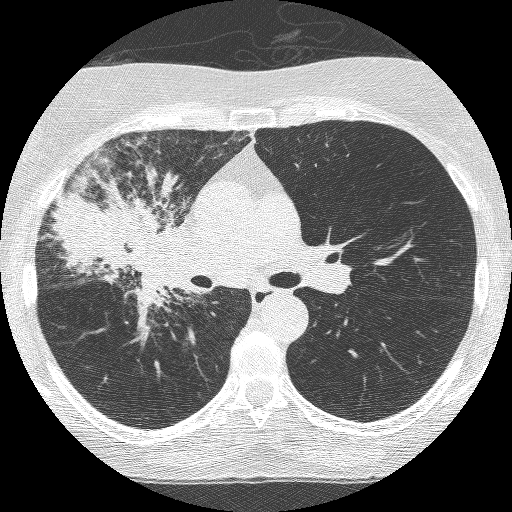
Low-dose screening chest CT, axial slice, third annual screen, lung window (W 1500 / L -600 HU), 1.25 mm slice thickness, lung (sharp) reconstruction kernel (BONE), 120 kVp, slice 155 of 253 in the series. Female, age 64 years at enrolment. Former smoker at enrolment.
Lesion marked by an expert reader, bounding box <74,193,203,323> (left, top, right, bottom; pixels). The exam's reader record, not a measurement of the box and not confirmed to be the same lesion: non-calcified nodule or mass ≥4 mm, right upper lobe, 49 × 43 mm, spiculated (stellate) margins, soft tissue attenuation, pre-existing on the prior screen: yes; interval growth: yes. Official screen result: positive, other. Participant outcome: lung cancer diagnosed 7 days after this screen — adenocarcinoma, NOS, right upper lobe, right middle lobe, right hilum, stage IV (AJCC 6th edition), 85 mm at pathology.